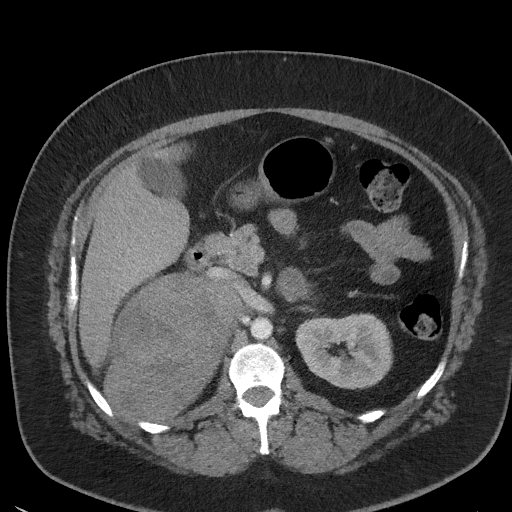
Contrast-enhanced abdominal CT, one axial slice; slice 27 of 56 in the series (ordered by position); reconstruction kernel I41f/3; 120 kVp; intravenous contrast given; soft-tissue window (W 400 / L 40 HU); 5 mm slice thickness; 512 × 512 image matrix, field of view 373 × 373 mm. Female patient, age 35 years. Case-level facts recorded for this patient, not image findings: diagnosis: adrenocortical carcinoma; tumour side: right adrenal; tumour size at pathology: 15 cm.
Outlined on this slice (semi-automatically segmented with operator editing):
- mass: bounding box (x1, y1, x2, y2) in pixels: (109, 275, 235, 418)